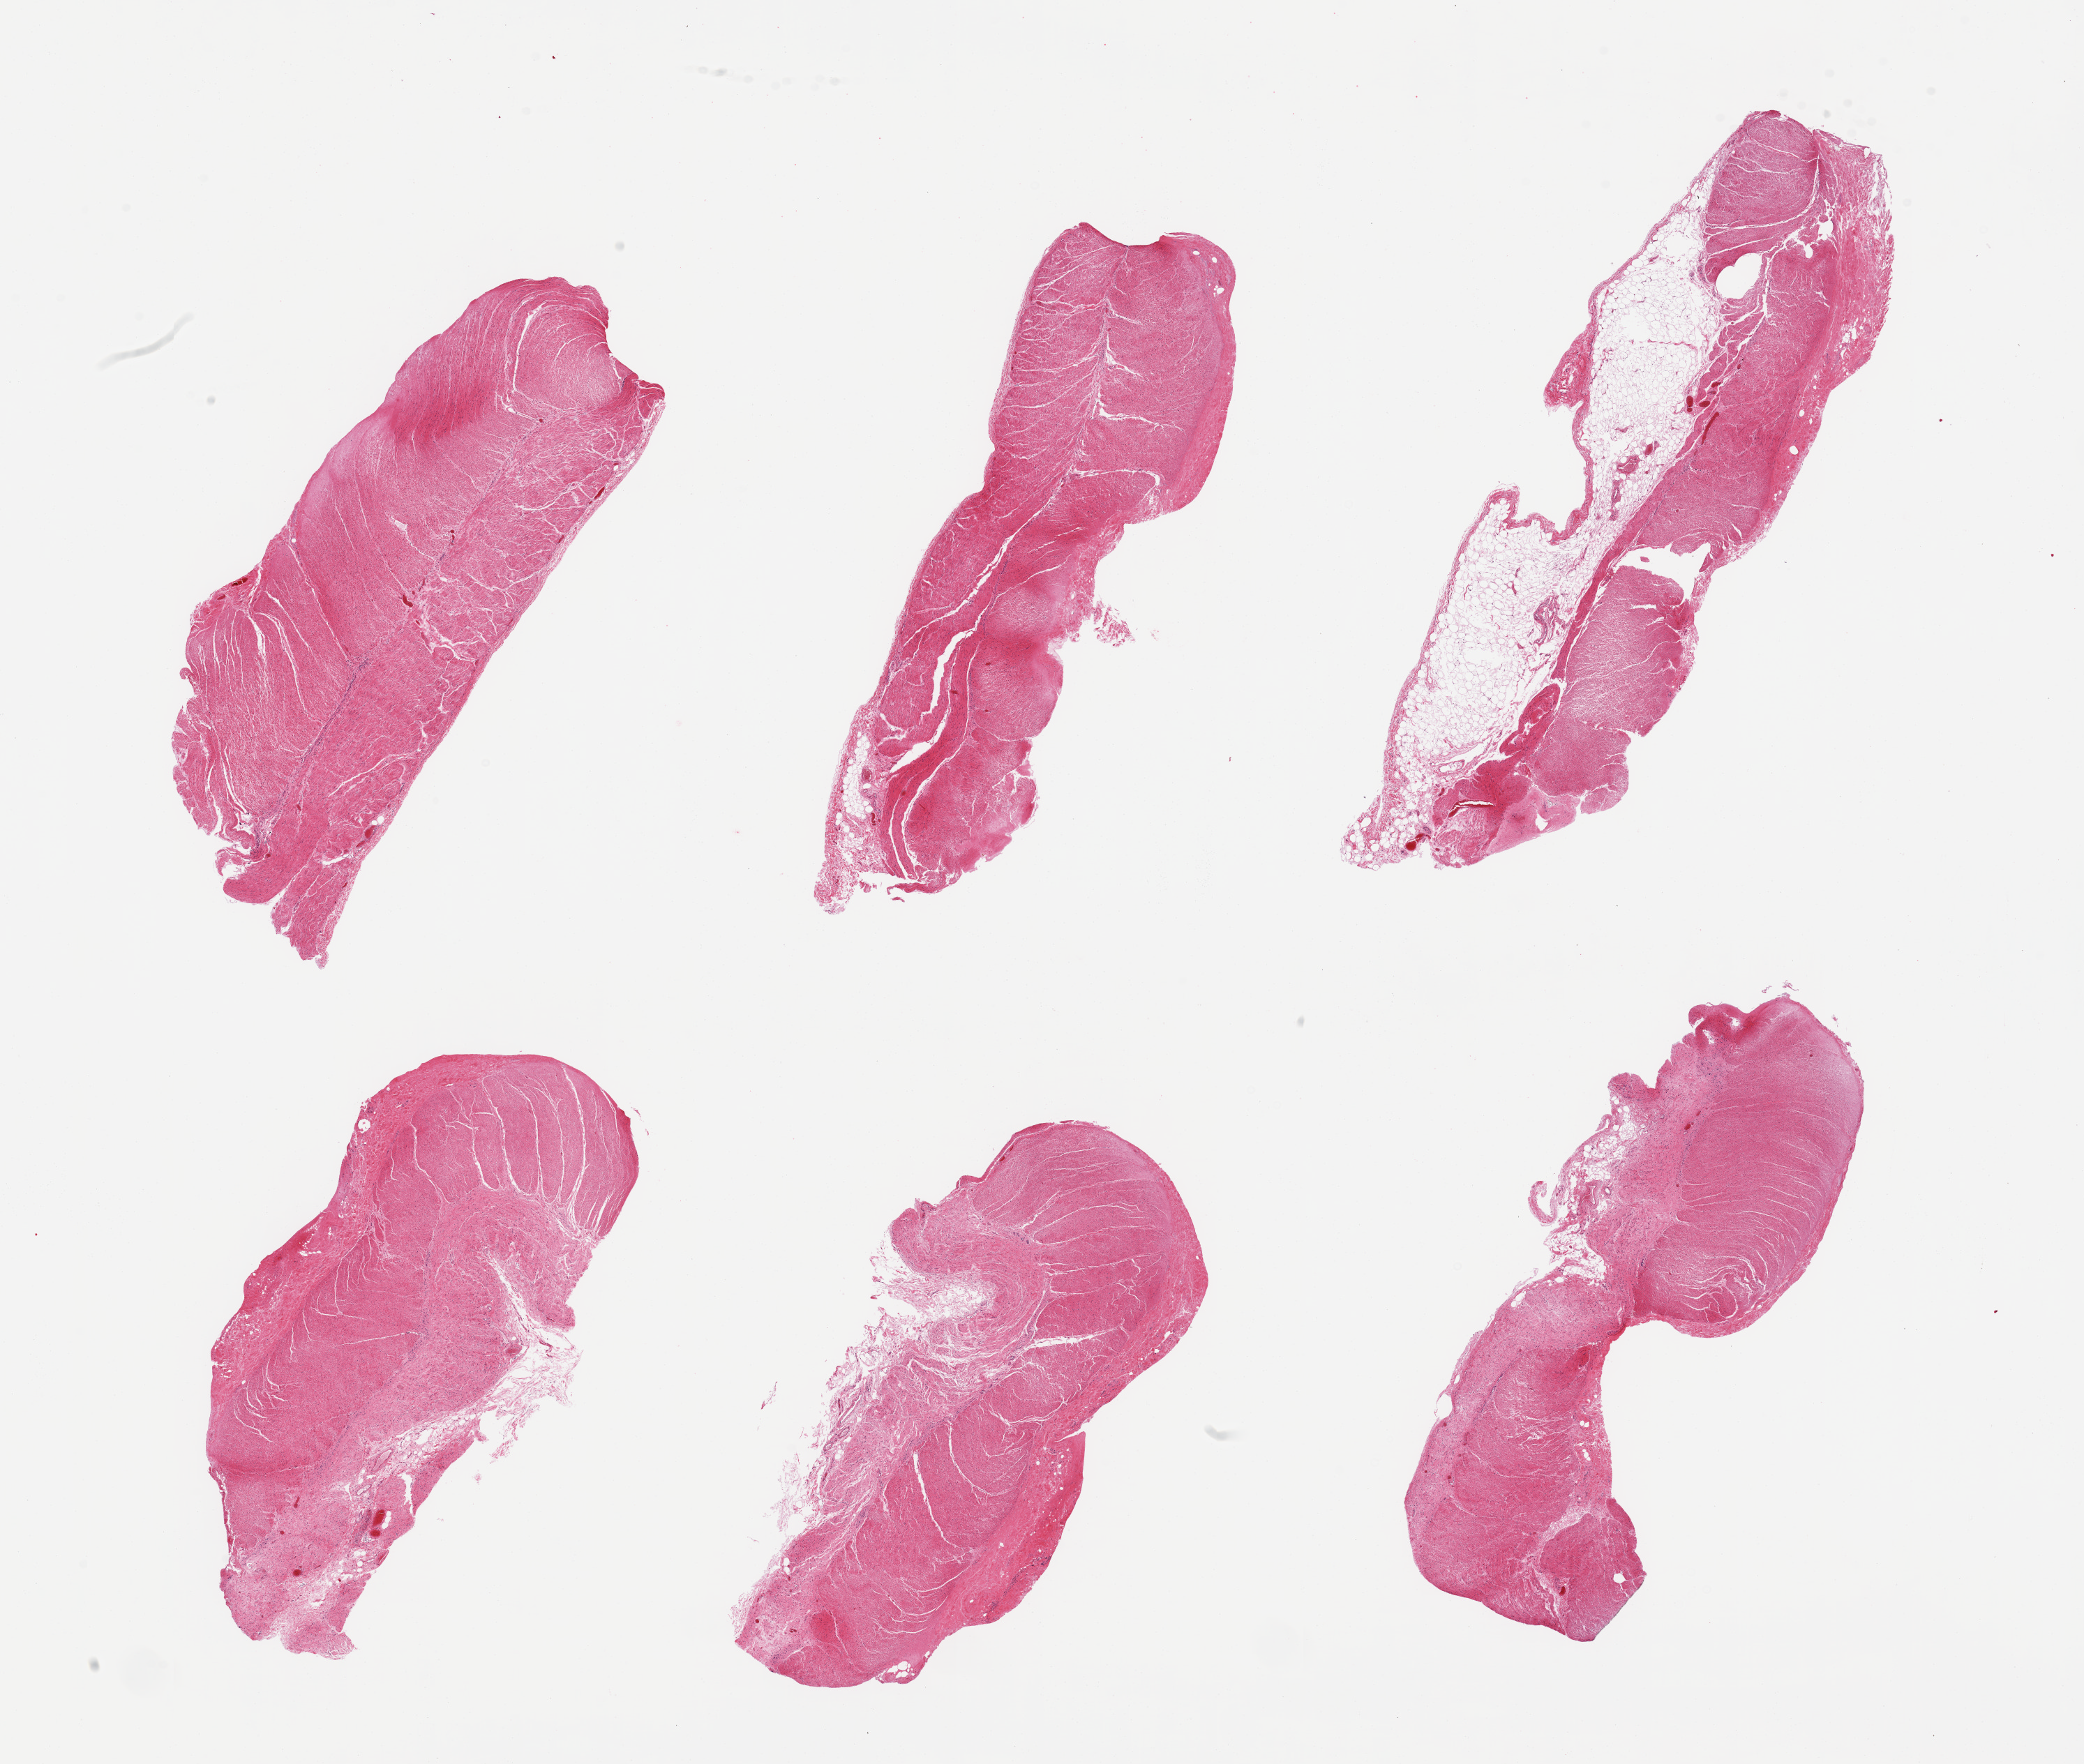
Haematoxylin and eosin whole-slide image — low-resolution overview of the scanned area, about 23.6 x 20.0 mm (acquisition: 20x scan); PAXgene-fixed paraffin-embedded (PFPE) section; sampled site (target tissue): sigmoid colon; donor tissue sample. Male donor.
• review note (as recorded): 6 pieces; 1 piece has 50% pericolonic fat